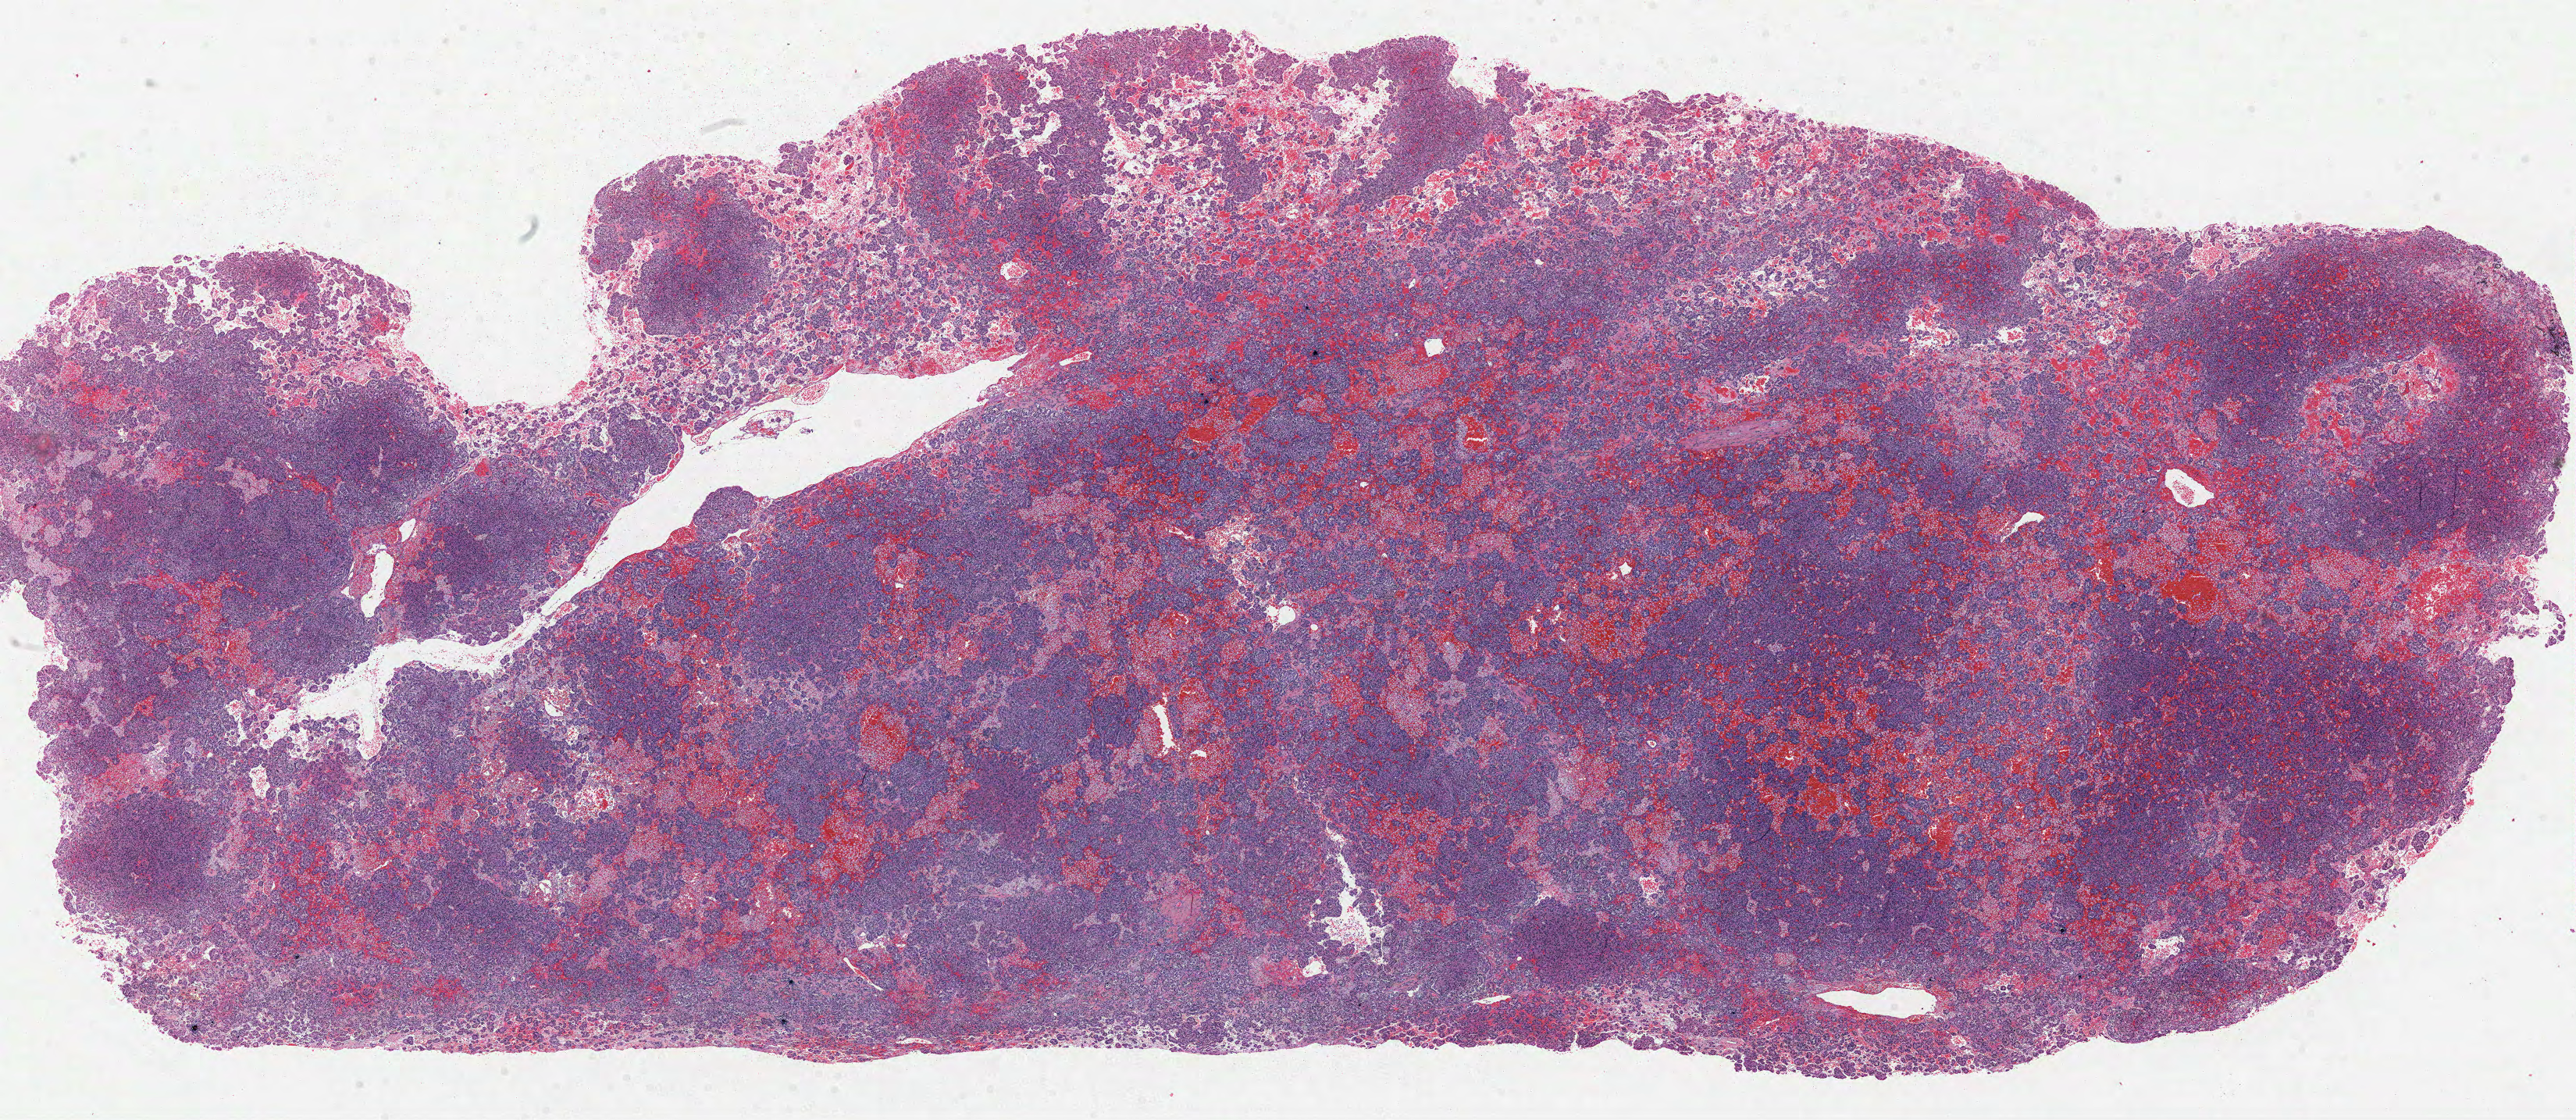
Digitized Hematoxylin and eosin (H&E) stained tissue section (whole slide), low-resolution overview of the scanned area, about 26.6 x 11.6 mm (from a 40x scan), FFPE section, primary tumour sample from the kidney. Female, age 48 years at initial diagnosis.
• laterality: left
• pathologic diagnosis: Papillary adenocarcinoma, NOS